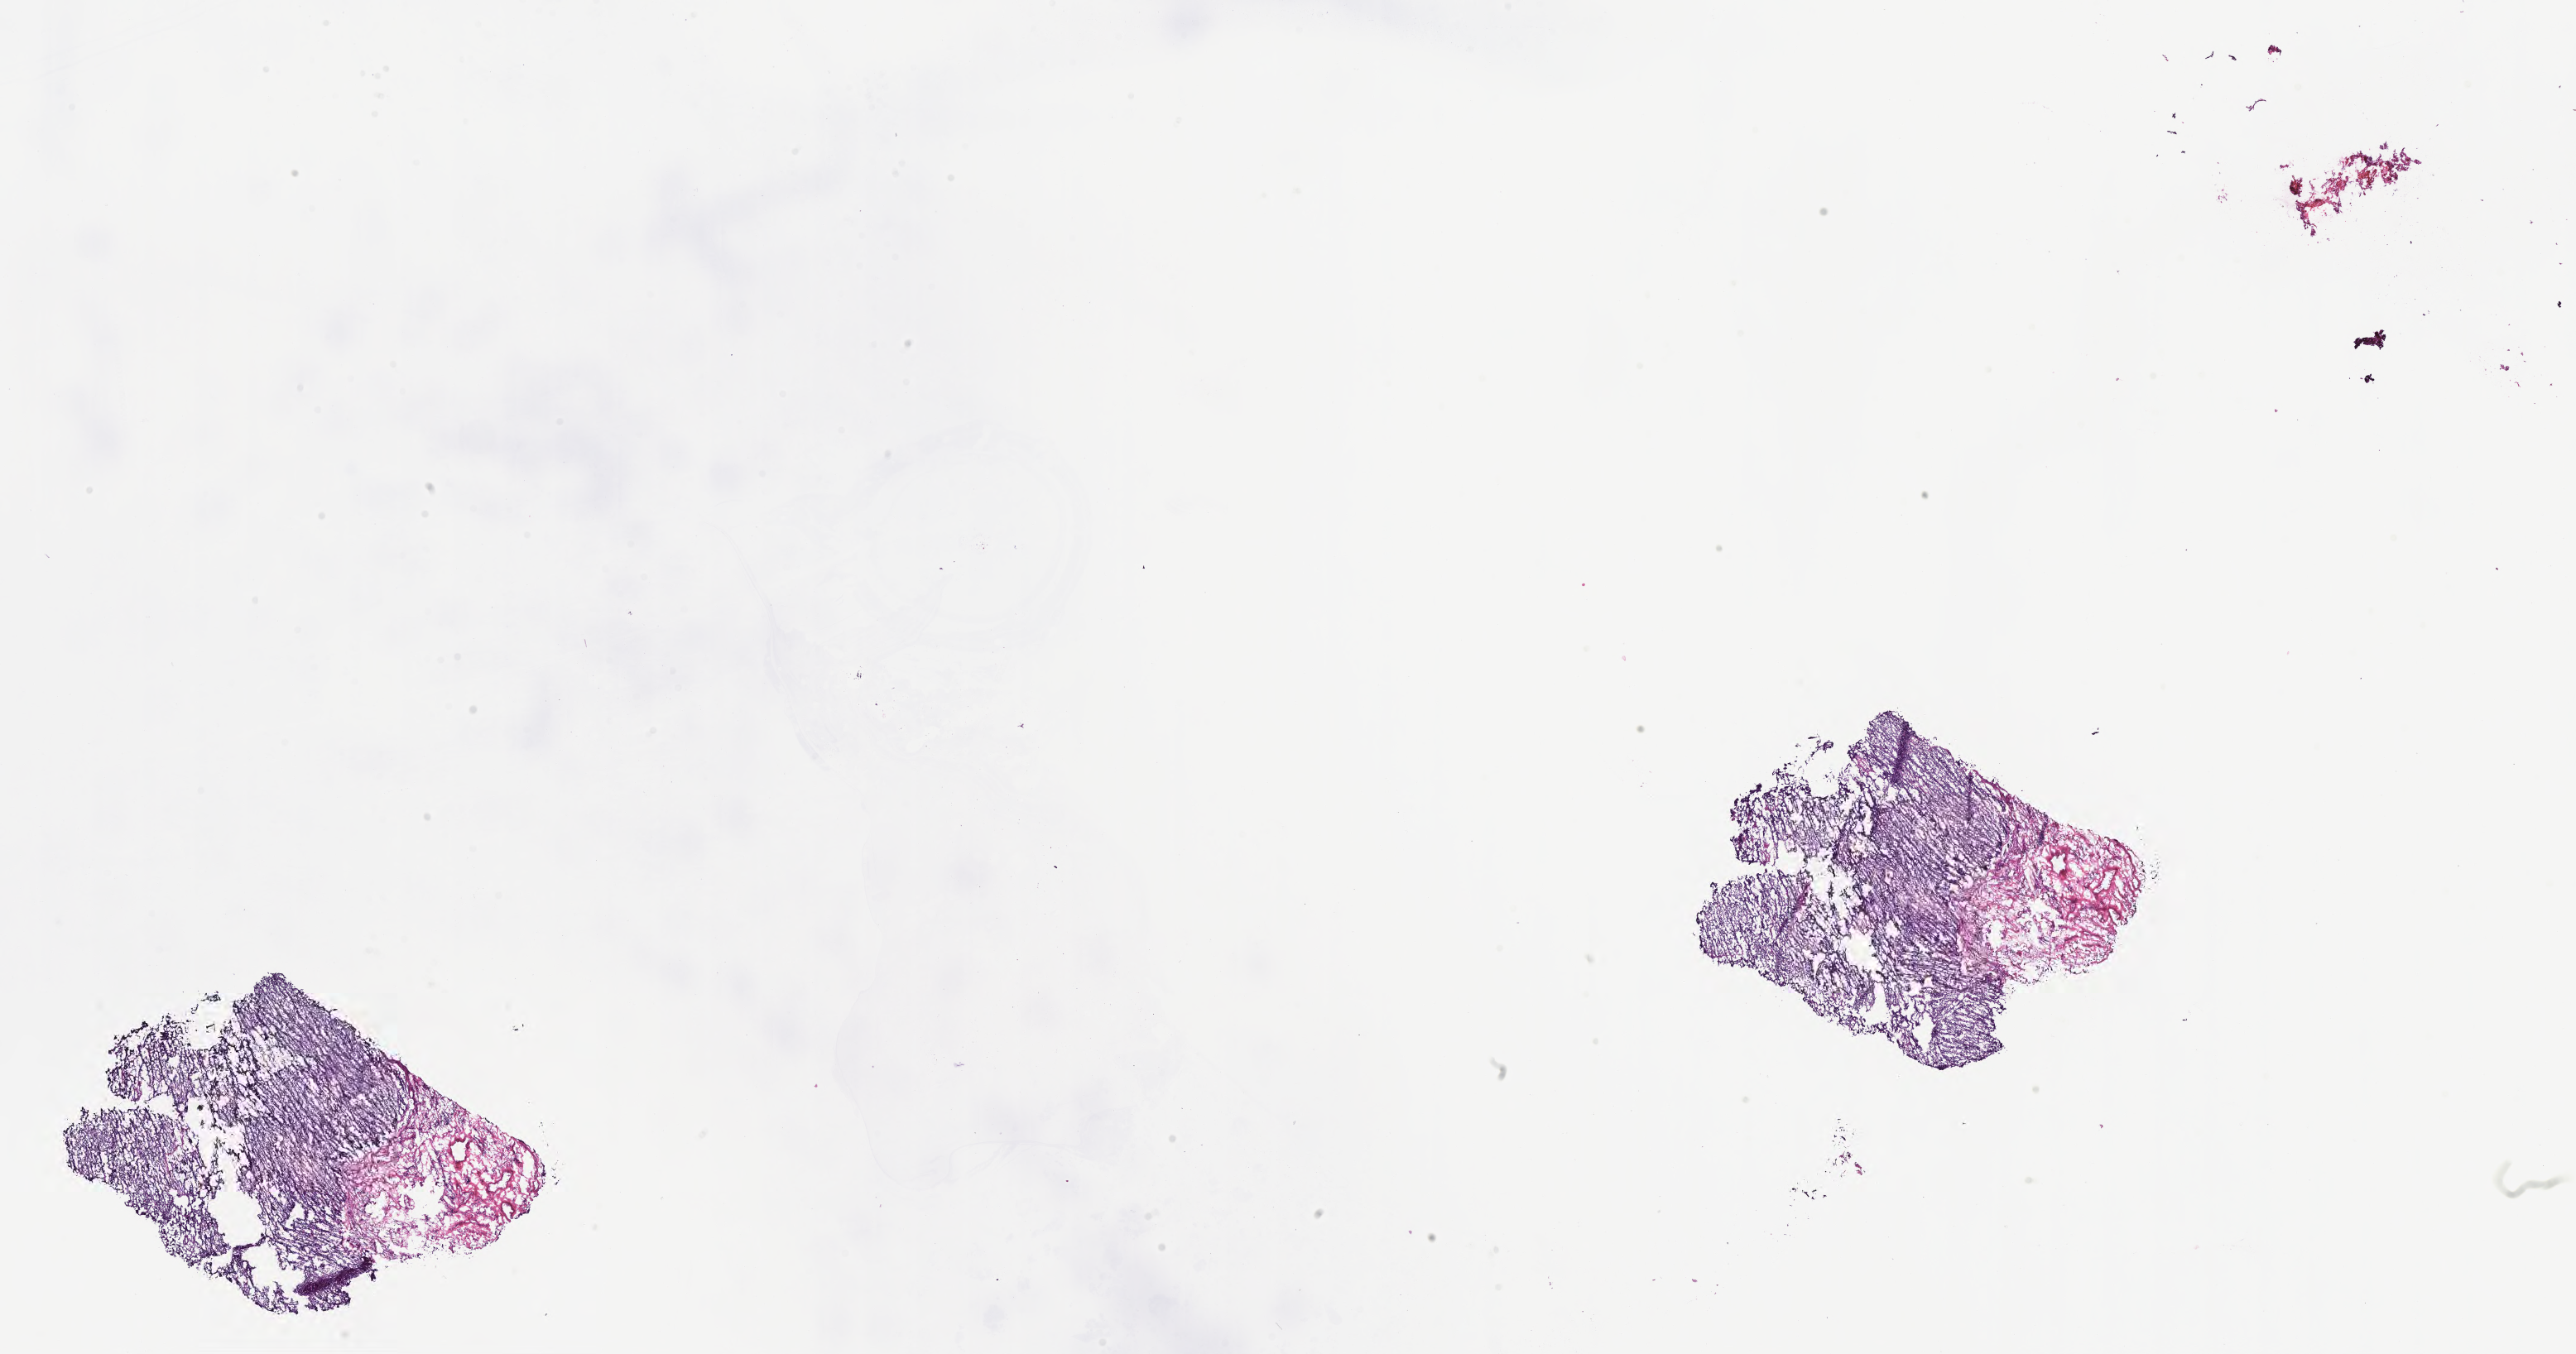
Whole-slide image, H&E stain of tumor tissue from the mediastinum, low-resolution overview of the scanned area, about 25.2 x 13.2 mm, cryosection (OCT / tissue freezing medium). Patient female; age 165 months (13 years 9 months).
Diagnosis (ICD-O-3 morphology term): Rhabdomyosarcoma, NOS.